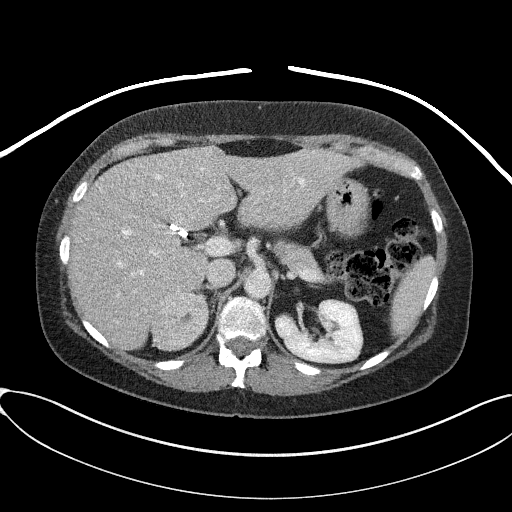
Contrast-enhanced abdominal CT, one axial slice. Position 55 of 95 along the scan axis. Reconstruction kernel I41f/2. Intravenous contrast given. Soft-tissue window (W 400 / L 40 HU). 512 × 512 image matrix, field of view 410 × 410 mm. Patient: female, 46 years. From the clinical record (not read from this slice): diagnosis: adrenocortical carcinoma; tumour side: right adrenal; tumour size at pathology: 7.2 cm; Ki-67 index: 50 %; stage (as recorded): 4.
Outlined on this slice (semi-automatic segmentation, software-assisted and operator-edited):
- mass: box from (x=152, y=293) to (x=207, y=350) px